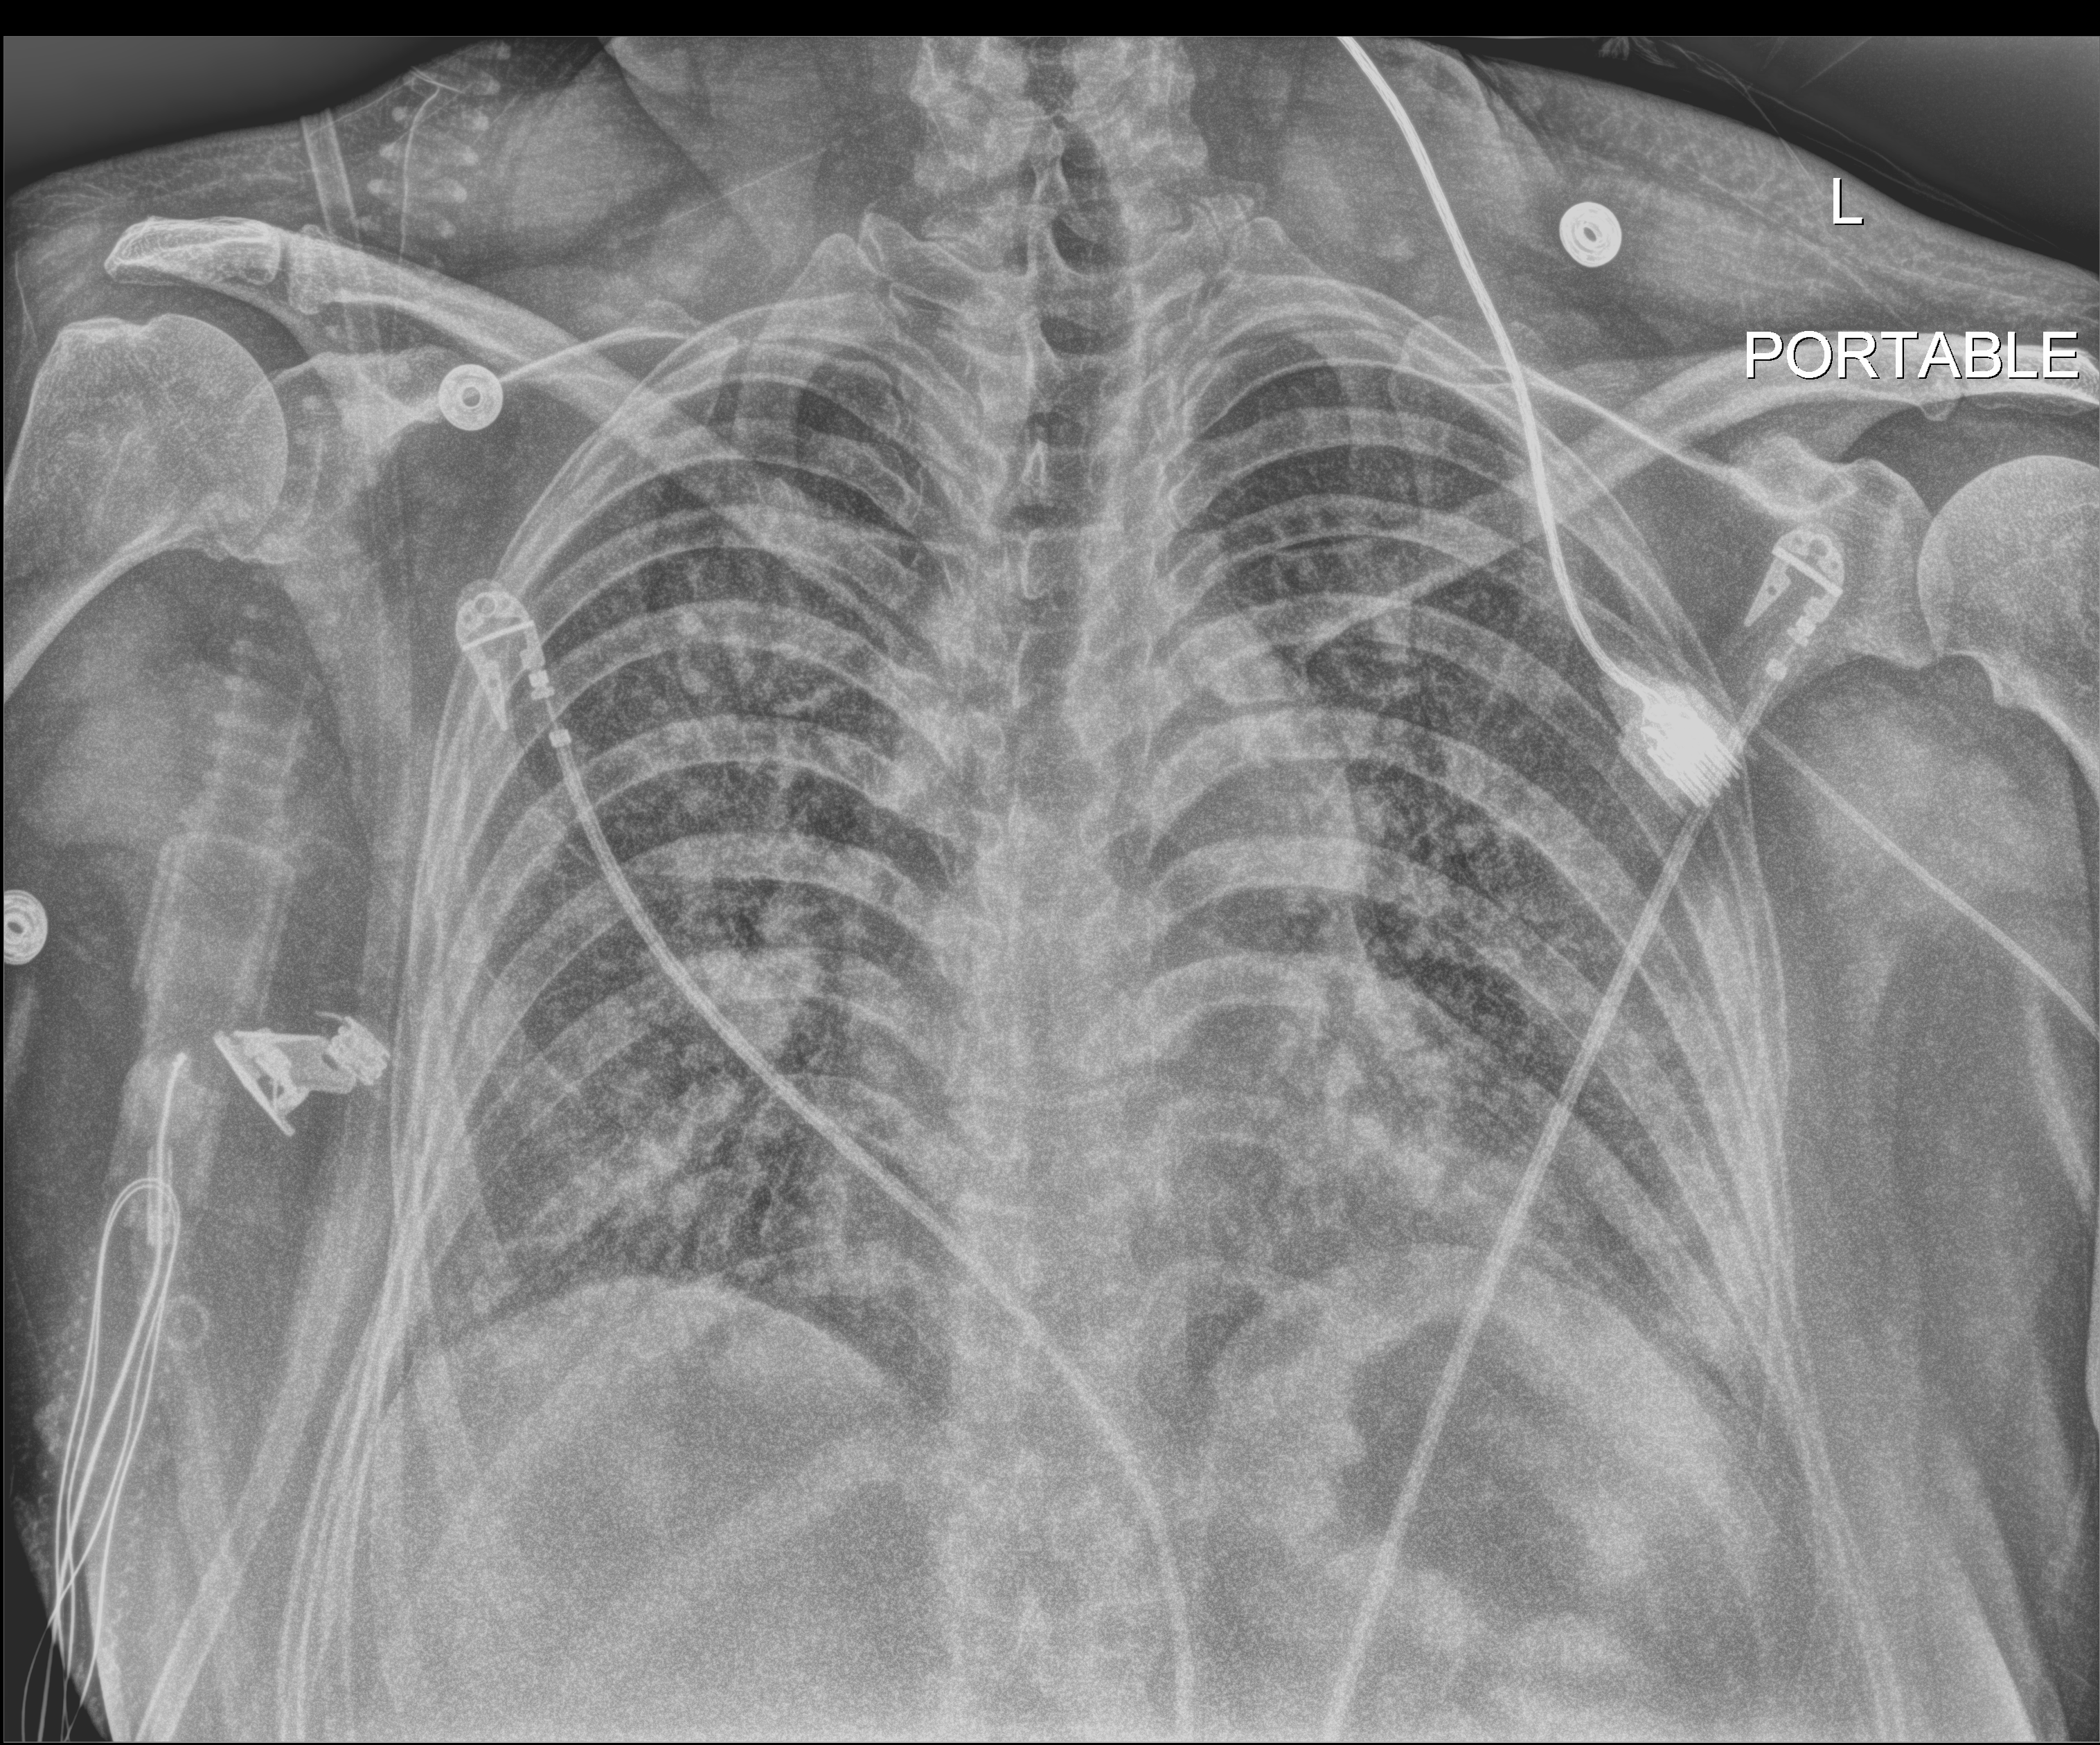
Portable chest radiograph; anteroposterior (AP) projection. Patient hospitalised with COVID-19, aged 18–59 years.
From the hospital-stay record, not from the radiograph (when in the stay this image was taken is not recorded): admitted to intensive care during this hospital stay: yes; smoking status (admission record): never; mechanically ventilated during this hospital stay: yes.